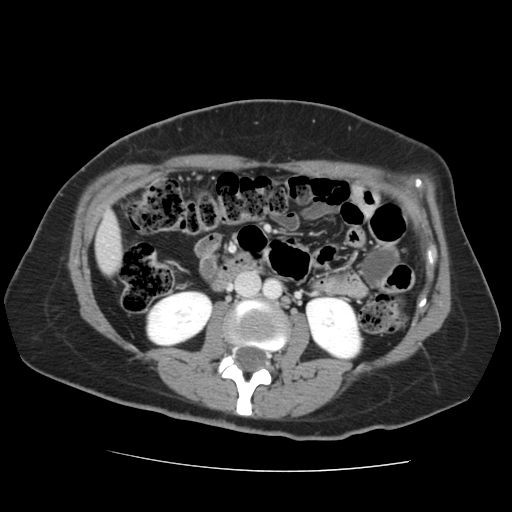
Contrast-enhanced abdominal CT, one axial slice; 120 kVp; intravenous contrast given; soft-tissue window (W 400 / L 40 HU); 2.5 mm slice thickness; 512 × 512 image matrix, field of view 333 × 333 mm. Female patient, age 46 years. From the clinical record (not read from this slice): diagnosis: colorectal cancer liver metastases, imaged before liver resection; multiple liver metastases: no; largest metastasis: 2.8 cm.
Annotated regions visible in this slice (outlined manually by an expert reader):
- liver: bounding box <96,217,123,274> (left, top, right, bottom; pixels)
- planned liver remnant (the part of the liver to remain after resection): <96,217,123,270>